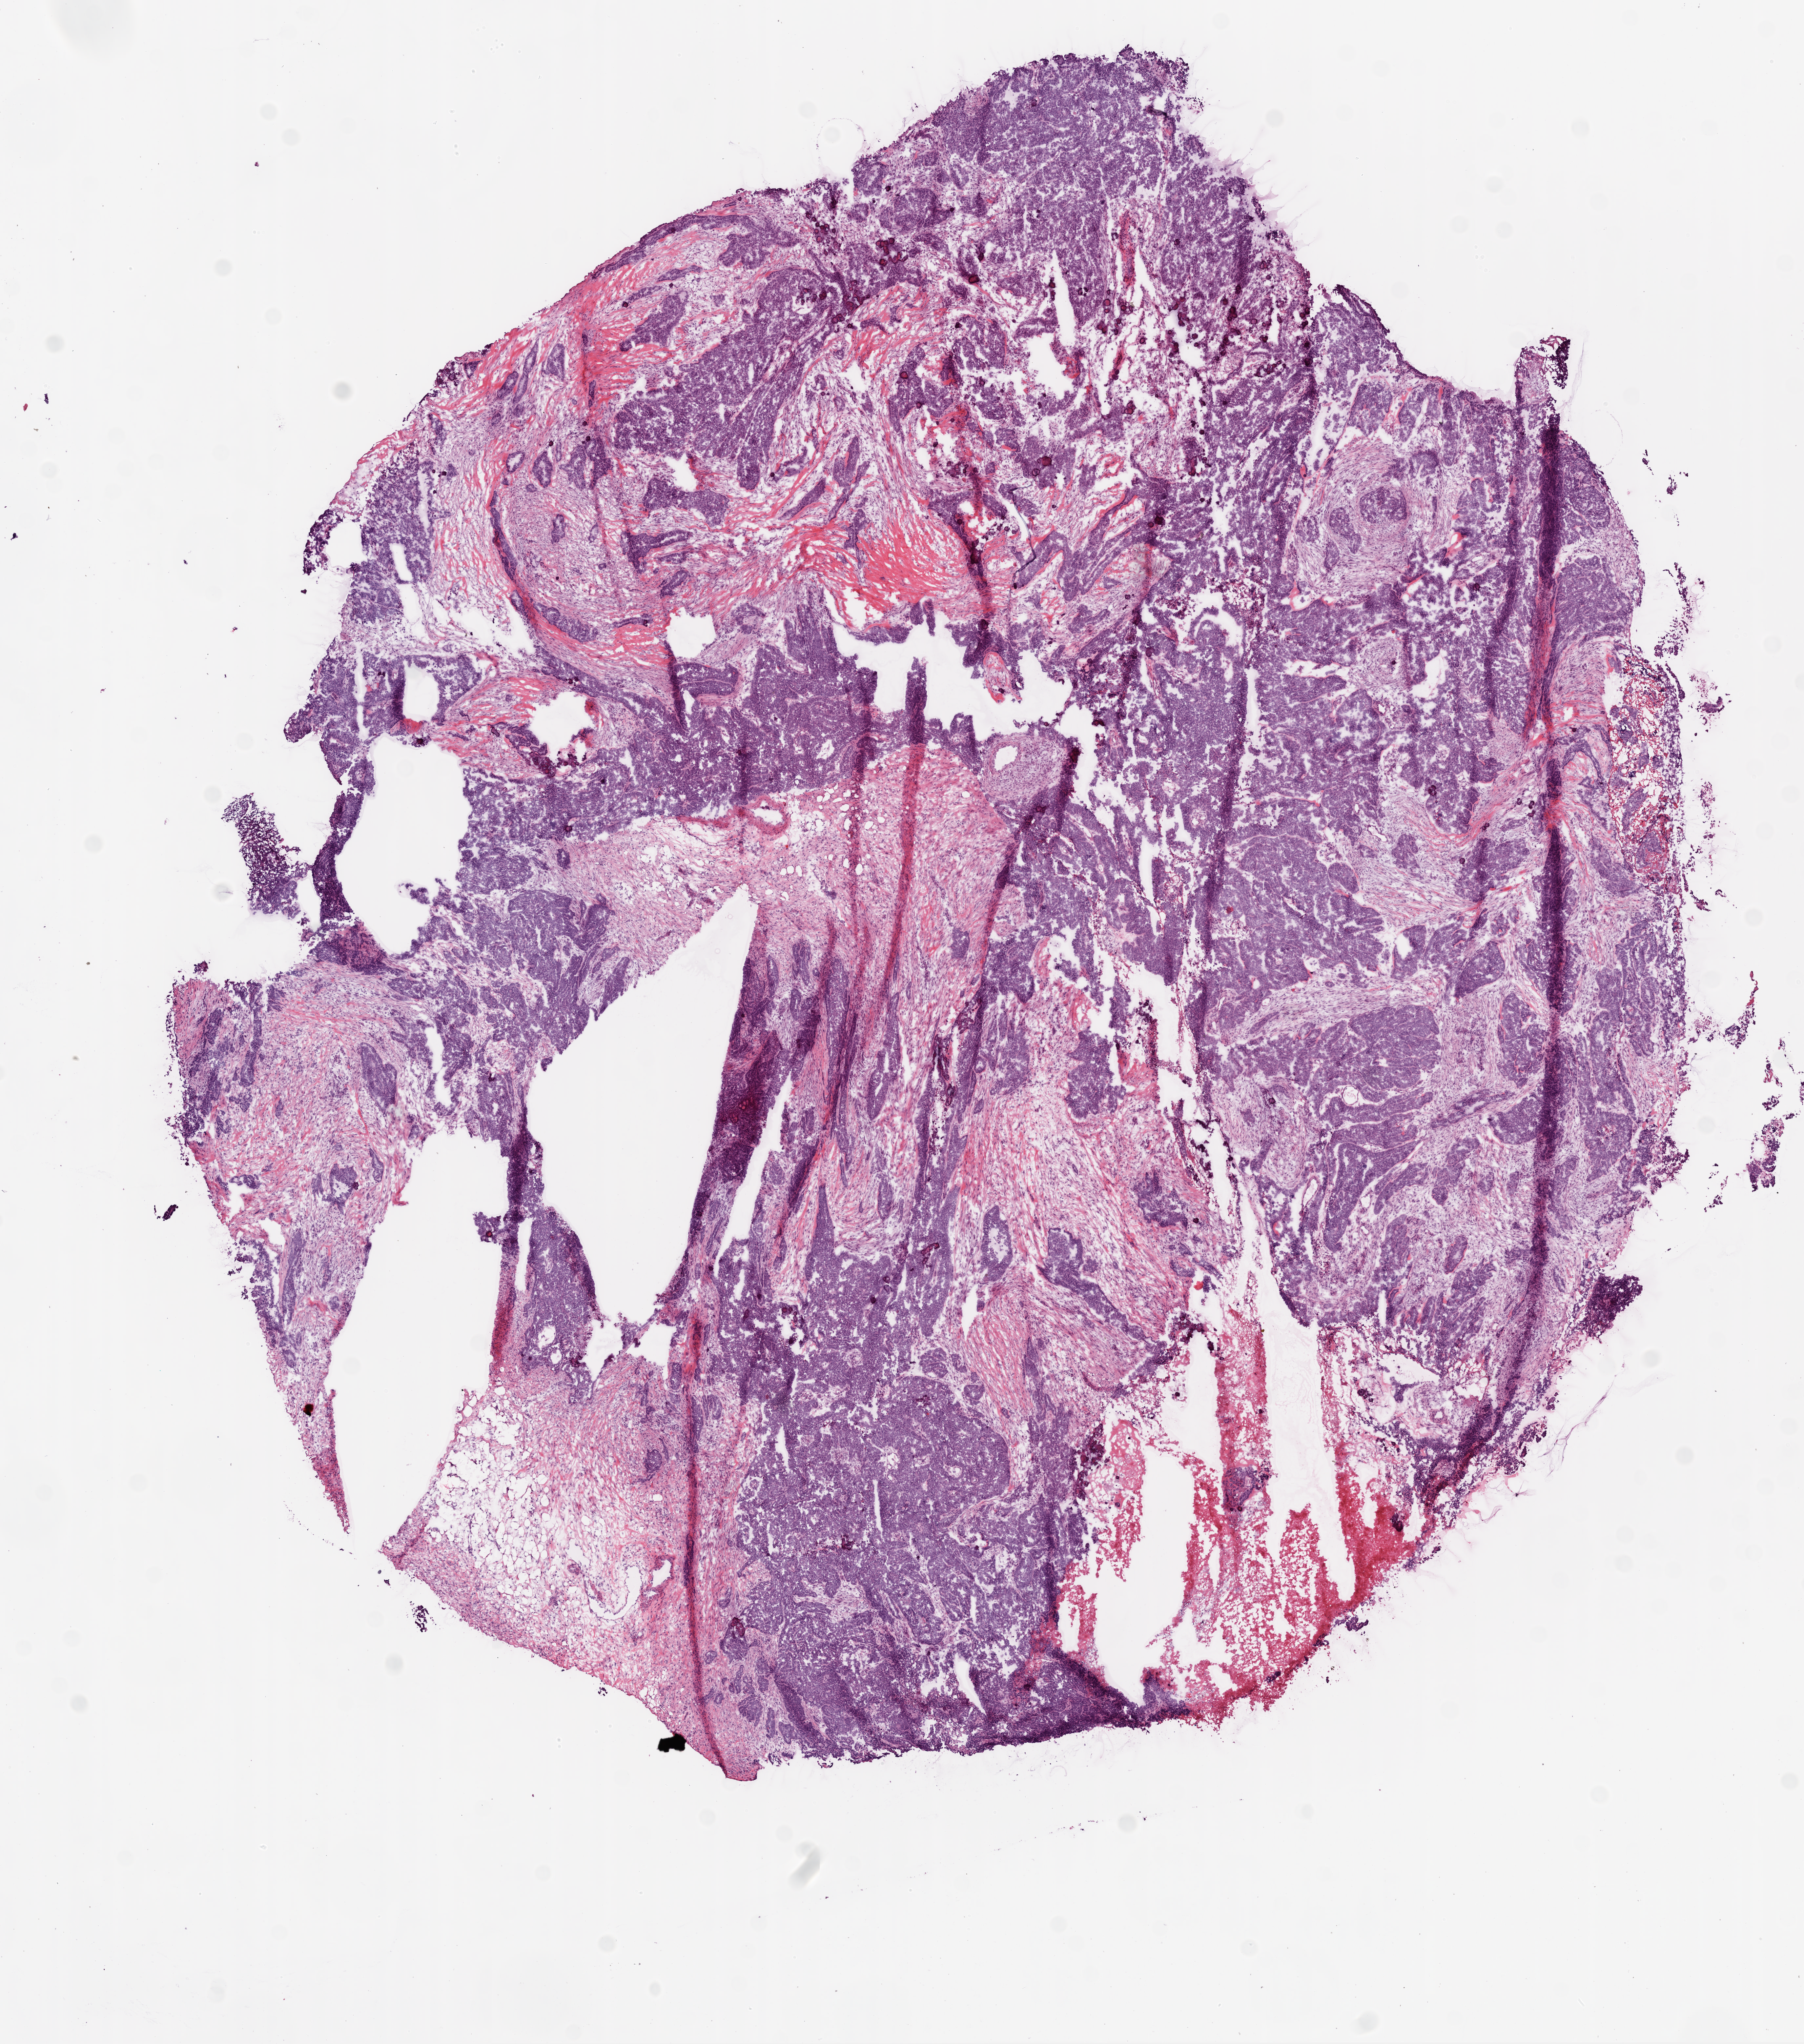
Digitized H&E tissue section (whole slide) — low-resolution overview of the scanned area, about 11.0 x 12.5 mm, frozen section from the bottom of the tissue portion, primary tumour sample from the ovary. Female, age 75 years at initial diagnosis. Histologic grade: G2 (moderately differentiated). Pathologist review of this section (percent, as recorded): tumour cells 49%, tumour nuclei 70%, normal cells 45%, stromal cells 0%, necrosis 6%.
* FIGO stage: IIIC
* histologic diagnosis: Serous cystadenocarcinoma, NOS